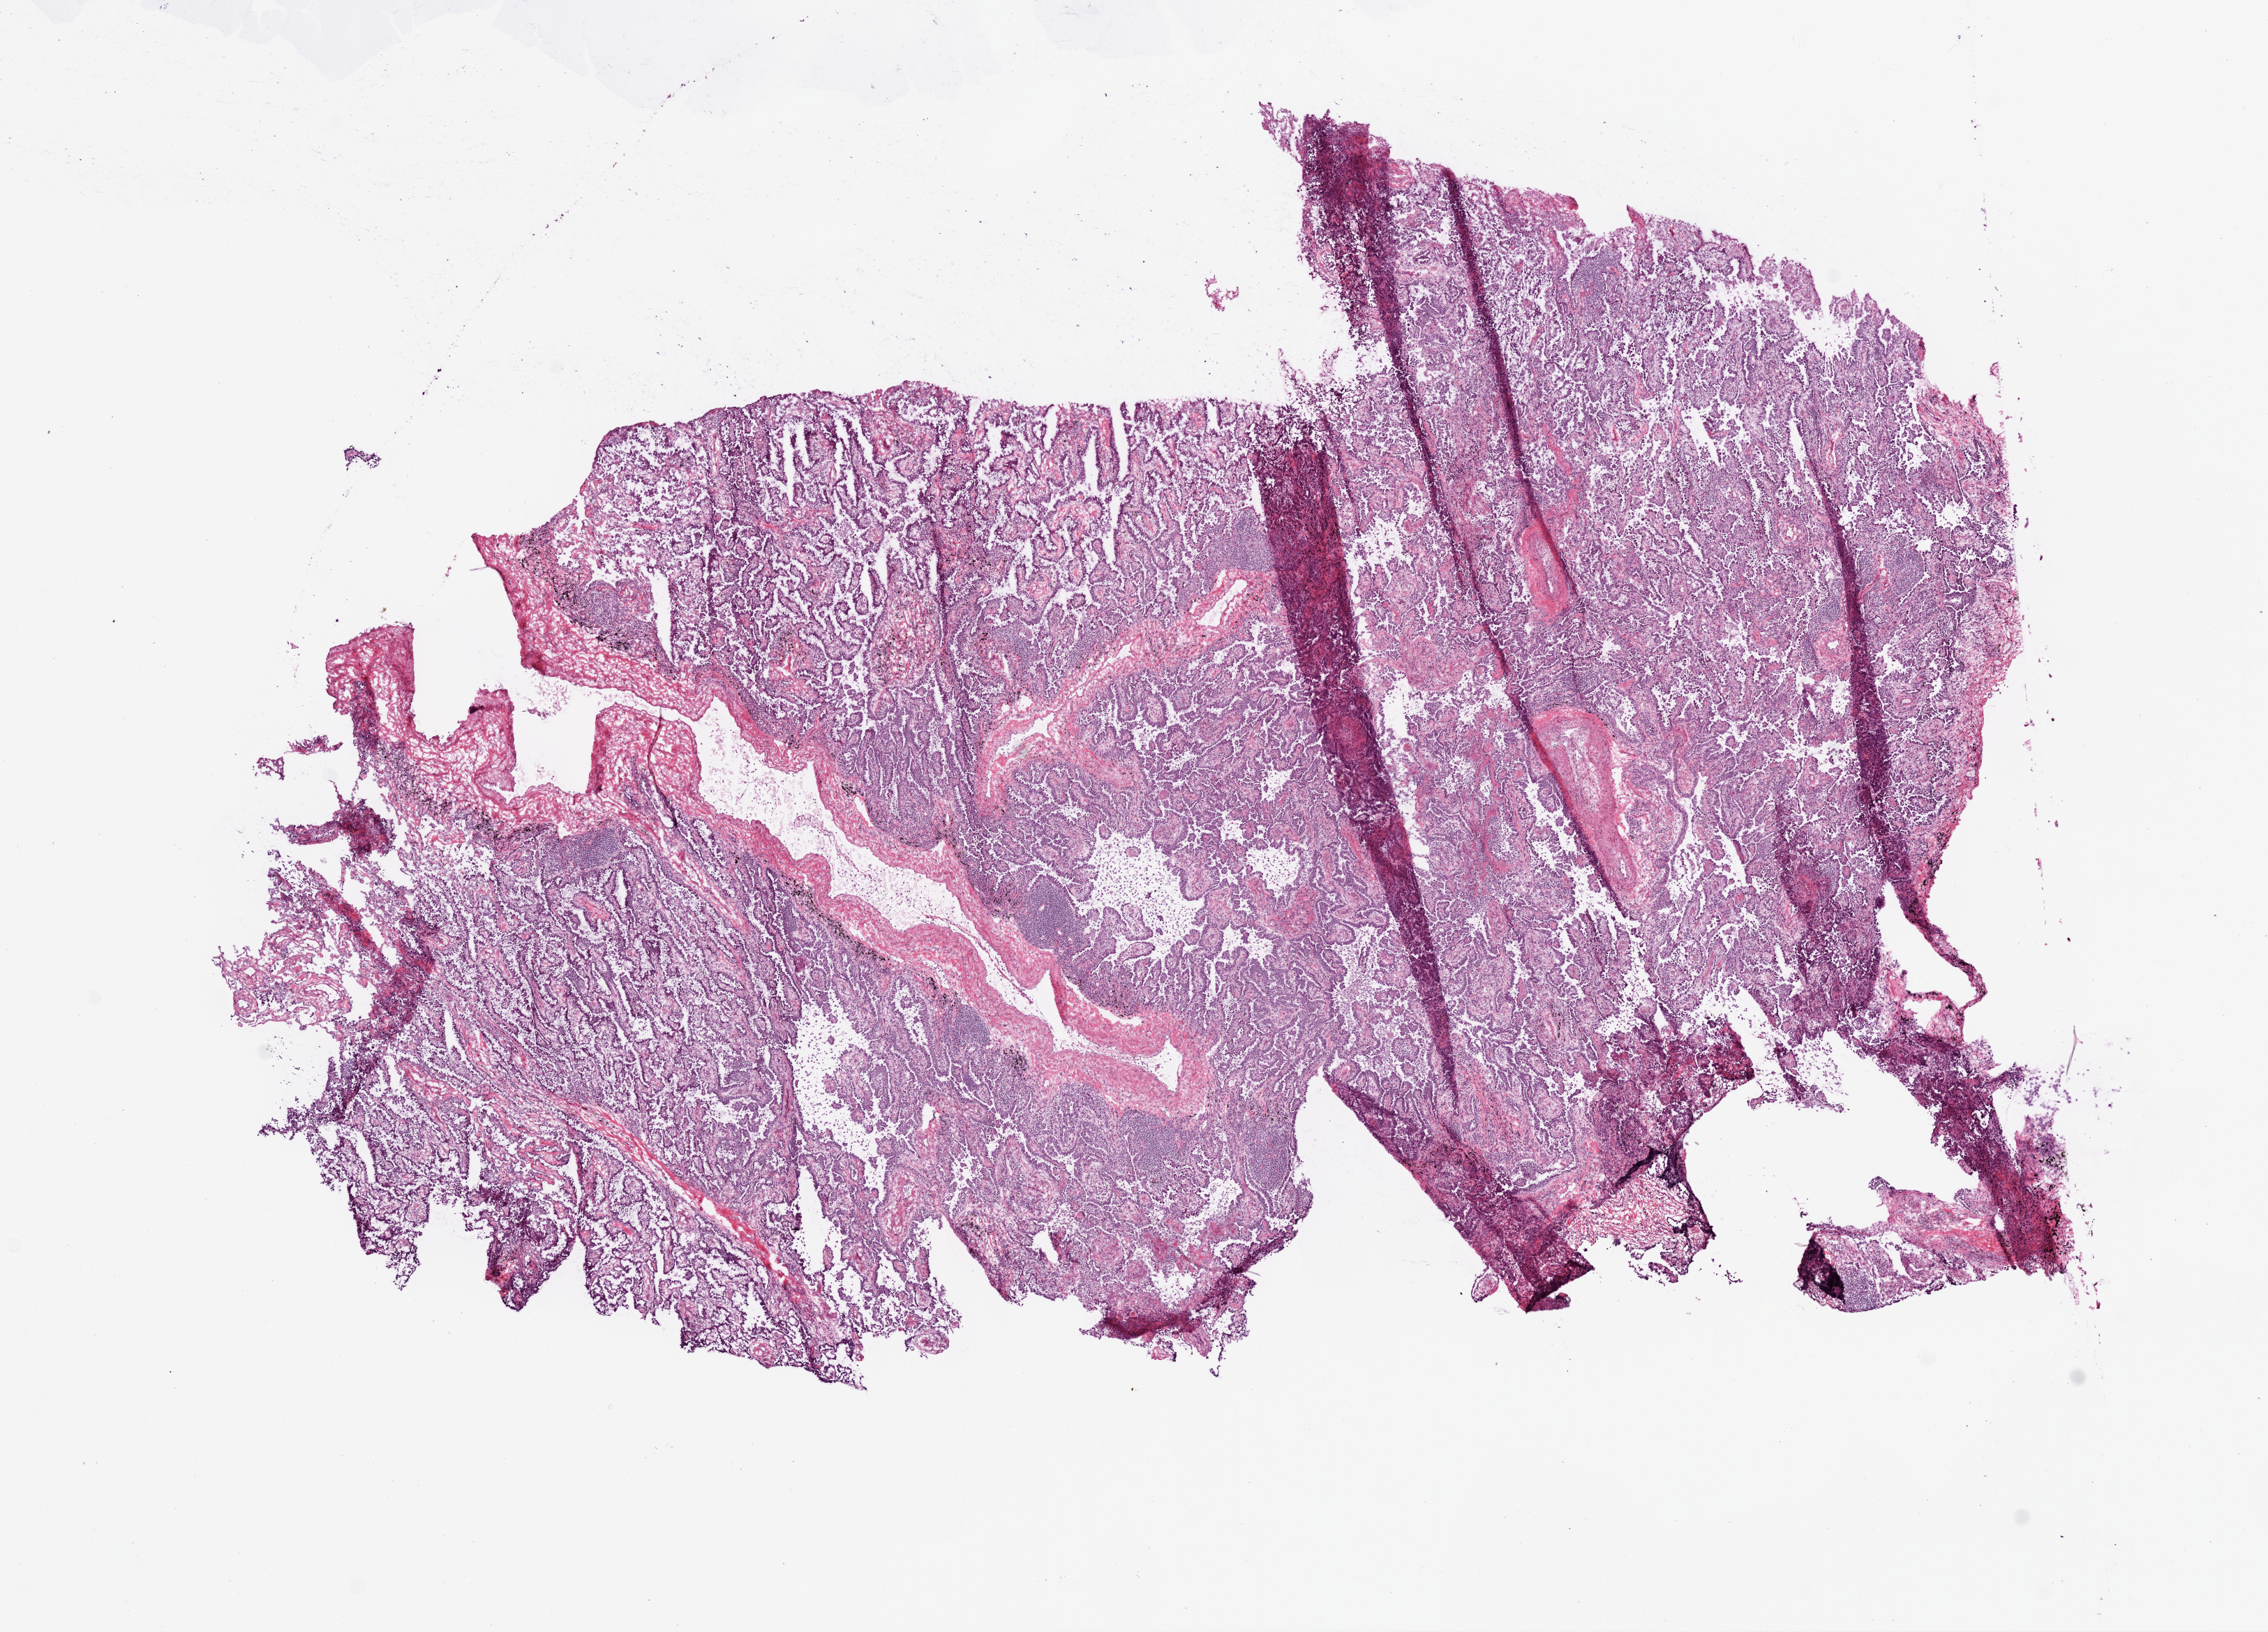
Whole-slide histology image, Hematoxylin and eosin (H&E) stained — shown as a low-resolution overview of the whole scanned area (about 13.0 x 9.4 mm, slide scanned at 20x), frozen section from the bottom of the tissue portion, lung, primary tumour sample. Male, age 67 years at initial diagnosis. Slide review estimates, as recorded: tumour cells 80%, tumour nuclei 80%, normal cells 0%, stromal cells 20%, necrosis 0%.
* AJCC pathologic stage: IB (6th edition)
* pathologic diagnosis: Adenocarcinoma, NOS (lower lobe, lung)
* laterality: right